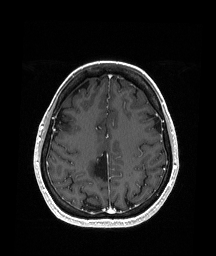
Brain MRI from a brain-tumour surgery series, one axial slice. Slice 64 of 151 in the series (ordered by position). T1-weighted post-contrast. 1.05 mm slice thickness. 216 × 256 image matrix, field of view 211 × 250 mm. Case-level facts recorded for this patient, not image findings: histopathology: Oligodendroglioma; WHO grade: 2; IDH mutation: yes.
Outlined on this slice (outlined manually by an expert reader):
- previous resection cavity: bounding box <94,149,109,183> (left, top, right, bottom; pixels)